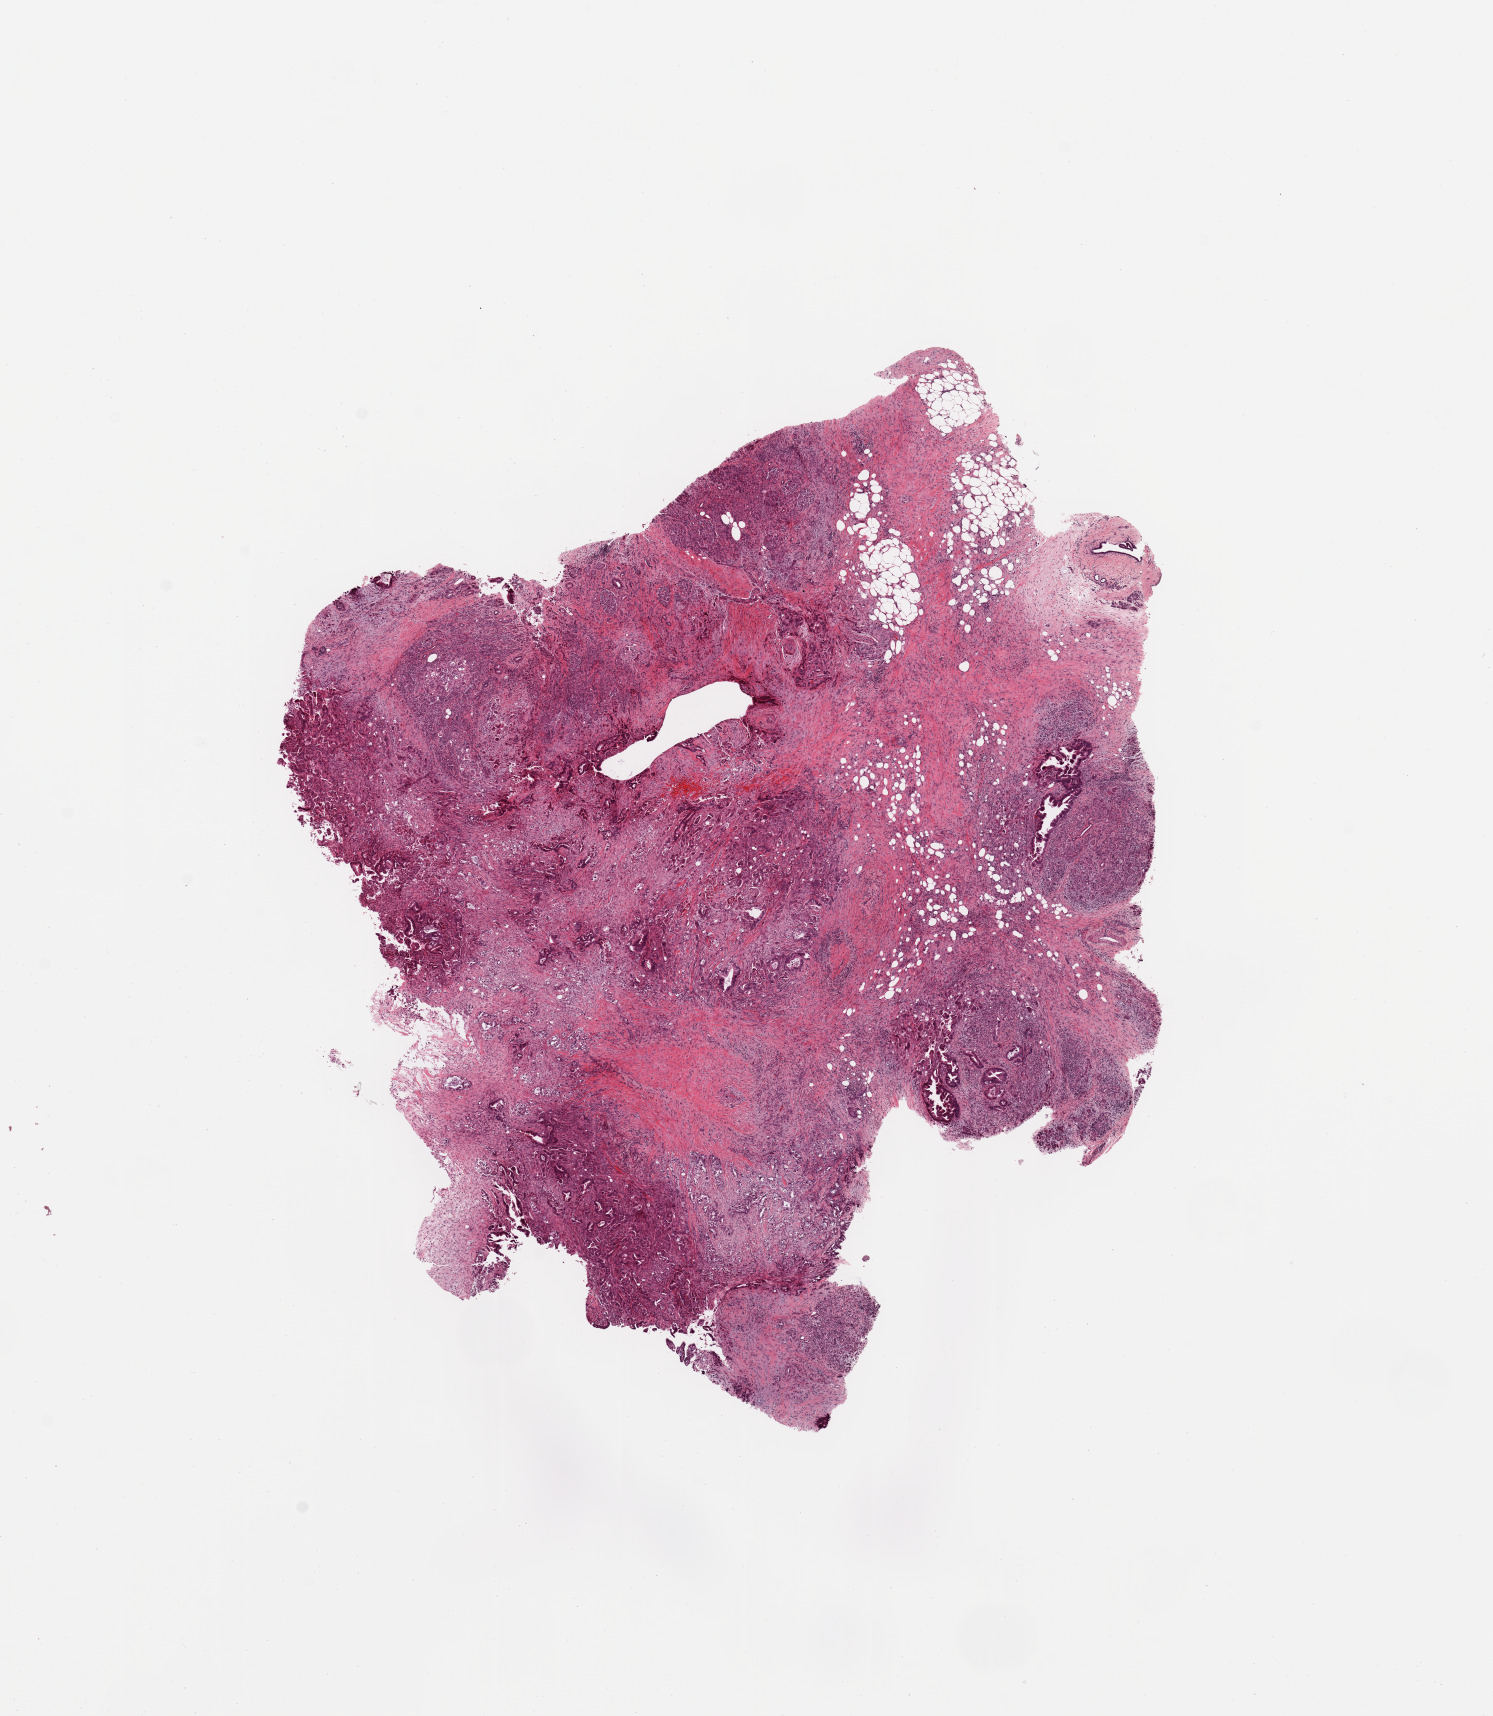
Digitized Hematoxylin and eosin (H&E) stained tissue section (whole slide), whole scanned area (about 11.8 x 13.6 mm, from a 20x scan) shown as a low-resolution overview. Pancreas, tumour tissue. Patient: male, age 74 years. Histologic grade: G3 (poorly differentiated).
Diagnosis: Infiltrating duct carcinoma, NOS. AJCC pathologic stage: IIB. Primary tumour site (as recorded): head.